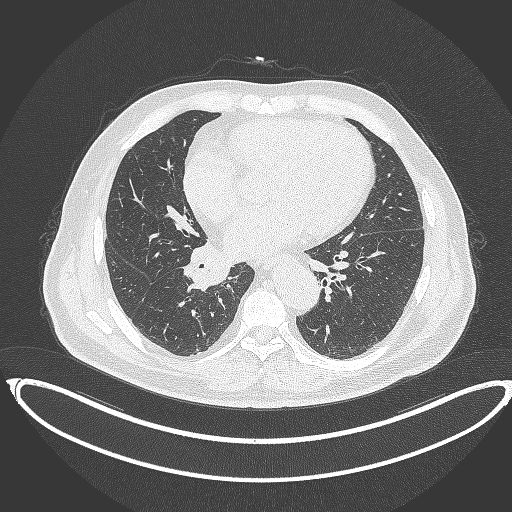
Chest CT, one axial slice; position 178 of 387 along the scan axis; reconstruction kernel B70f; 120 kVp; lung window (W 1500 / L -600 HU); 512 × 512 image matrix. Patient: male, 61 years. Case-level facts recorded for this patient, not image findings: clinical TNM (as recorded): T1b N1 M0.
Annotated regions visible in this slice (rectangle marked by the reading radiologist):
- lung tumour (recorded histology: squamous cell carcinoma): bounding box [x1, y1, x2, y2] px = [184, 236, 230, 294]